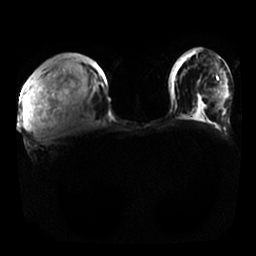
Breast MRI, one axial slice; slice 8 of 25 in the series (ordered by position); diffusion-weighted series; image 2 of 4 stored at this slice position (different b-values; order by instance number); 1.5 T; 256 × 256 image matrix, field of view 350 × 350 mm. Female patient.
Annotated regions visible in this slice (manually delineated by an expert):
- tumour on diffusion-weighted imaging: bounding box (x1, y1, x2, y2) in pixels: (23, 75, 47, 130)